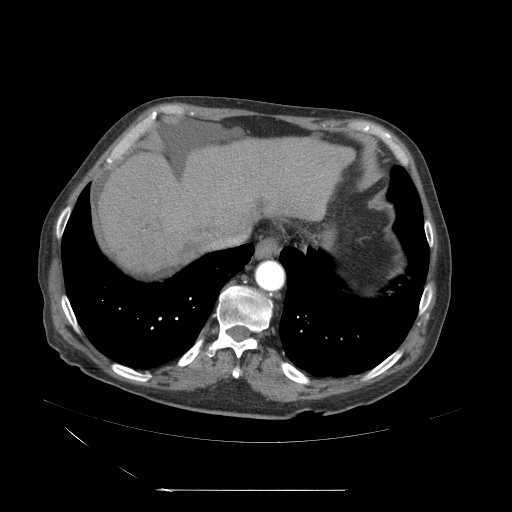
Contrast-enhanced abdominal CT (liver protocol), one axial slice. Slice 50 of 71 in the series (ordered by position). Soft-tissue window (W 400 / L 40 HU). 2.5 mm slice thickness. 512 × 512 image matrix. From the clinical record (not read from this slice): diagnosis: hepatocellular carcinoma (patient treated with transarterial chemoembolisation; whether this scan precedes or follows treatment is not stated here); TNM stage (as recorded): Stage-II.
Annotated regions visible in this slice (semi-automatic segmentation, software-assisted and operator-edited):
- abdominal aorta: box from (x=255, y=261) to (x=285, y=291) px
- liver parenchyma outside the tumour (the mass and vessels are separate outlines, so this box may not span the whole liver): (x=102, y=137)–(x=347, y=276)
- mass: (x=152, y=273)–(x=176, y=289)
- liver vessels: (x=103, y=194)–(x=243, y=257)